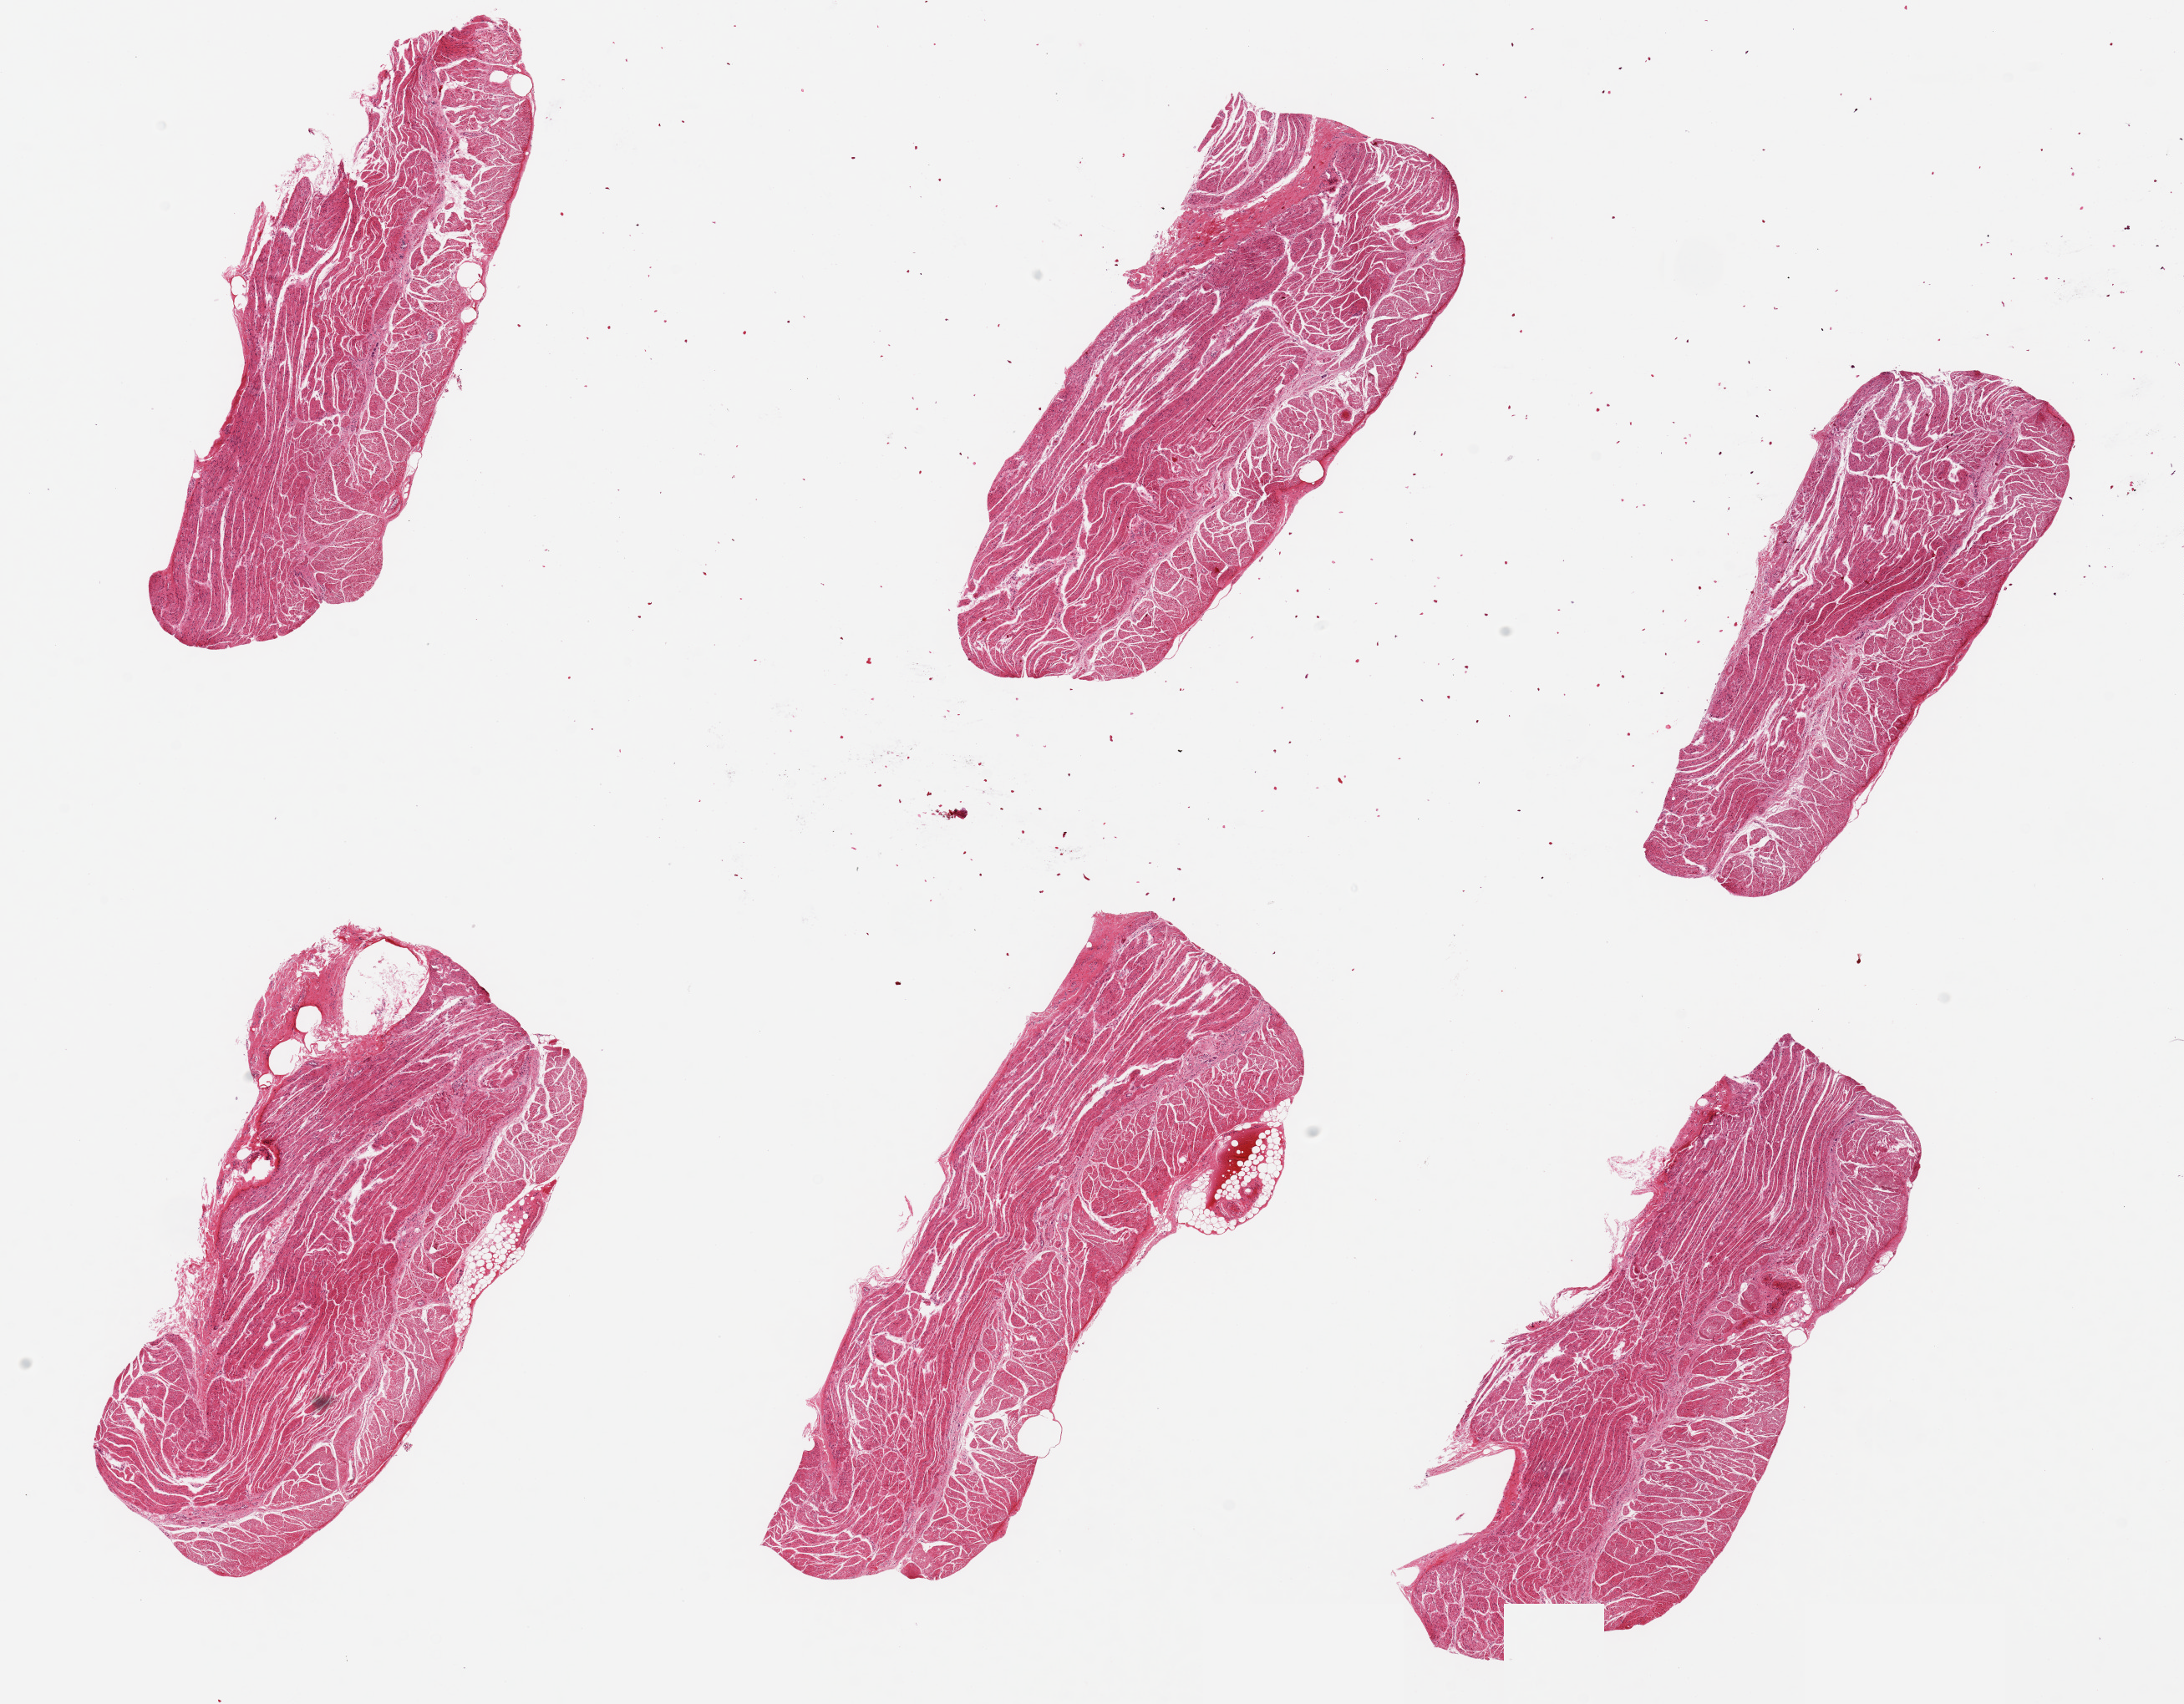
Haematoxylin and eosin whole-slide image, brightfield — shown as a low-resolution overview of the whole scanned area (about 20.7 x 16.1 mm). PAXgene-fixed, paraffin-embedded tissue. Sampled site (target tissue): esophageal muscle. Donor tissue sample. Male donor.
Pathologist's review note for this sample: 6 pieces, up to 7x3mm; well trimmed muscle.